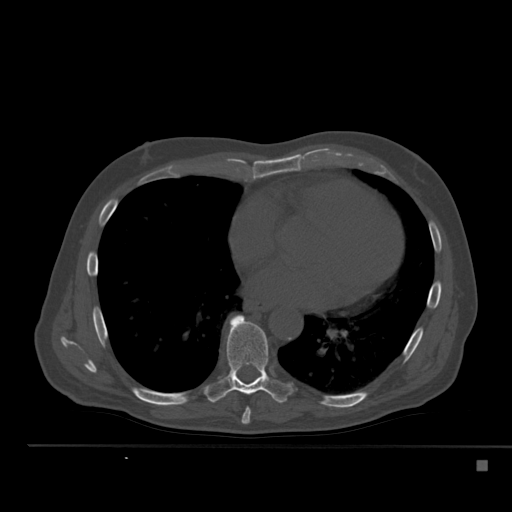
CT including the spine, one axial slice. Position 310 of 517 along the scan axis. Bone window (W 1800 / L 400 HU). 1.5 mm slice thickness. 512 × 512 image matrix, field of view 408 × 408 mm. Male patient, age 70 years. From the clinical record (not read from this slice): primary cancer: renal.
Annotated regions visible in this slice (semi-automatic segmentation, software-assisted and operator-edited):
- T7 vertebra: bounding box [x1, y1, x2, y2] px = [241, 407, 251, 424]
- T8 vertebra: [204, 315, 292, 403]